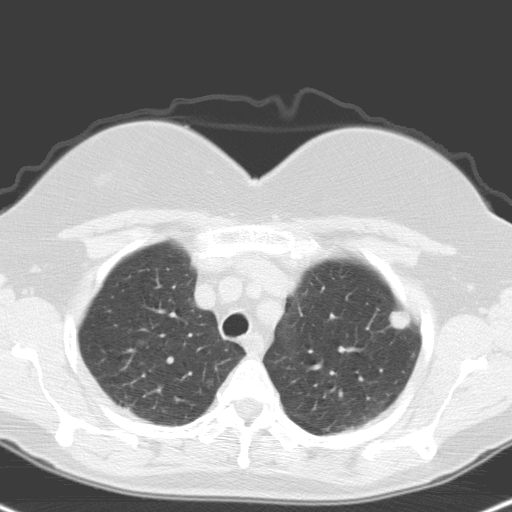
Low-dose screening chest CT, axial slice; first (baseline) screen; lung window (W 1500 / L -600 HU); 120 kVp; slice 23 of 148 in the series. Female participant, aged 59 years at enrolment. Current smoker at enrolment.
Expert-annotated lung lesion, box from (x=381, y=299) to (x=422, y=343) px. The screening reader recorded 2 non-calcified nodules or masses ≥4 mm on this exam (right upper lobe, left upper lobe); which of them this box marks is not recorded. Participant outcome: lung cancer diagnosed 48 days after this screen — large cell neuroendocrine carcinoma, left upper lobe, poorly differentiated (G3), stage IA (AJCC 6th edition), 12 mm at pathology.